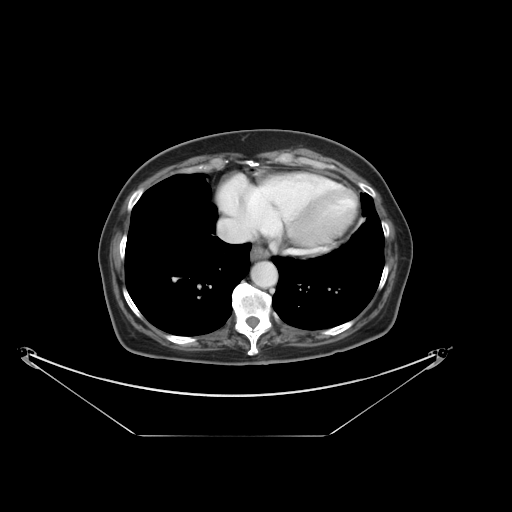
Contrast-enhanced abdominal CT, one axial slice. Slice 35 of 36 in the series (ordered by position). Intravenous contrast given. Soft-tissue window (W 400 / L 40 HU). 5 mm slice thickness. 512 × 512 image matrix, field of view 500 × 500 mm. Female patient, age 70 years. From the clinical record (not read from this slice): diagnosis: colorectal cancer liver metastases, imaged before liver resection; multiple liver metastases: no; largest metastasis: 2.5 cm; chemotherapy before resection: no.
Structures marked on this image (expert manual segmentation):
- hepatic veins: bounding box <219,210,237,242> (left, top, right, bottom; pixels)